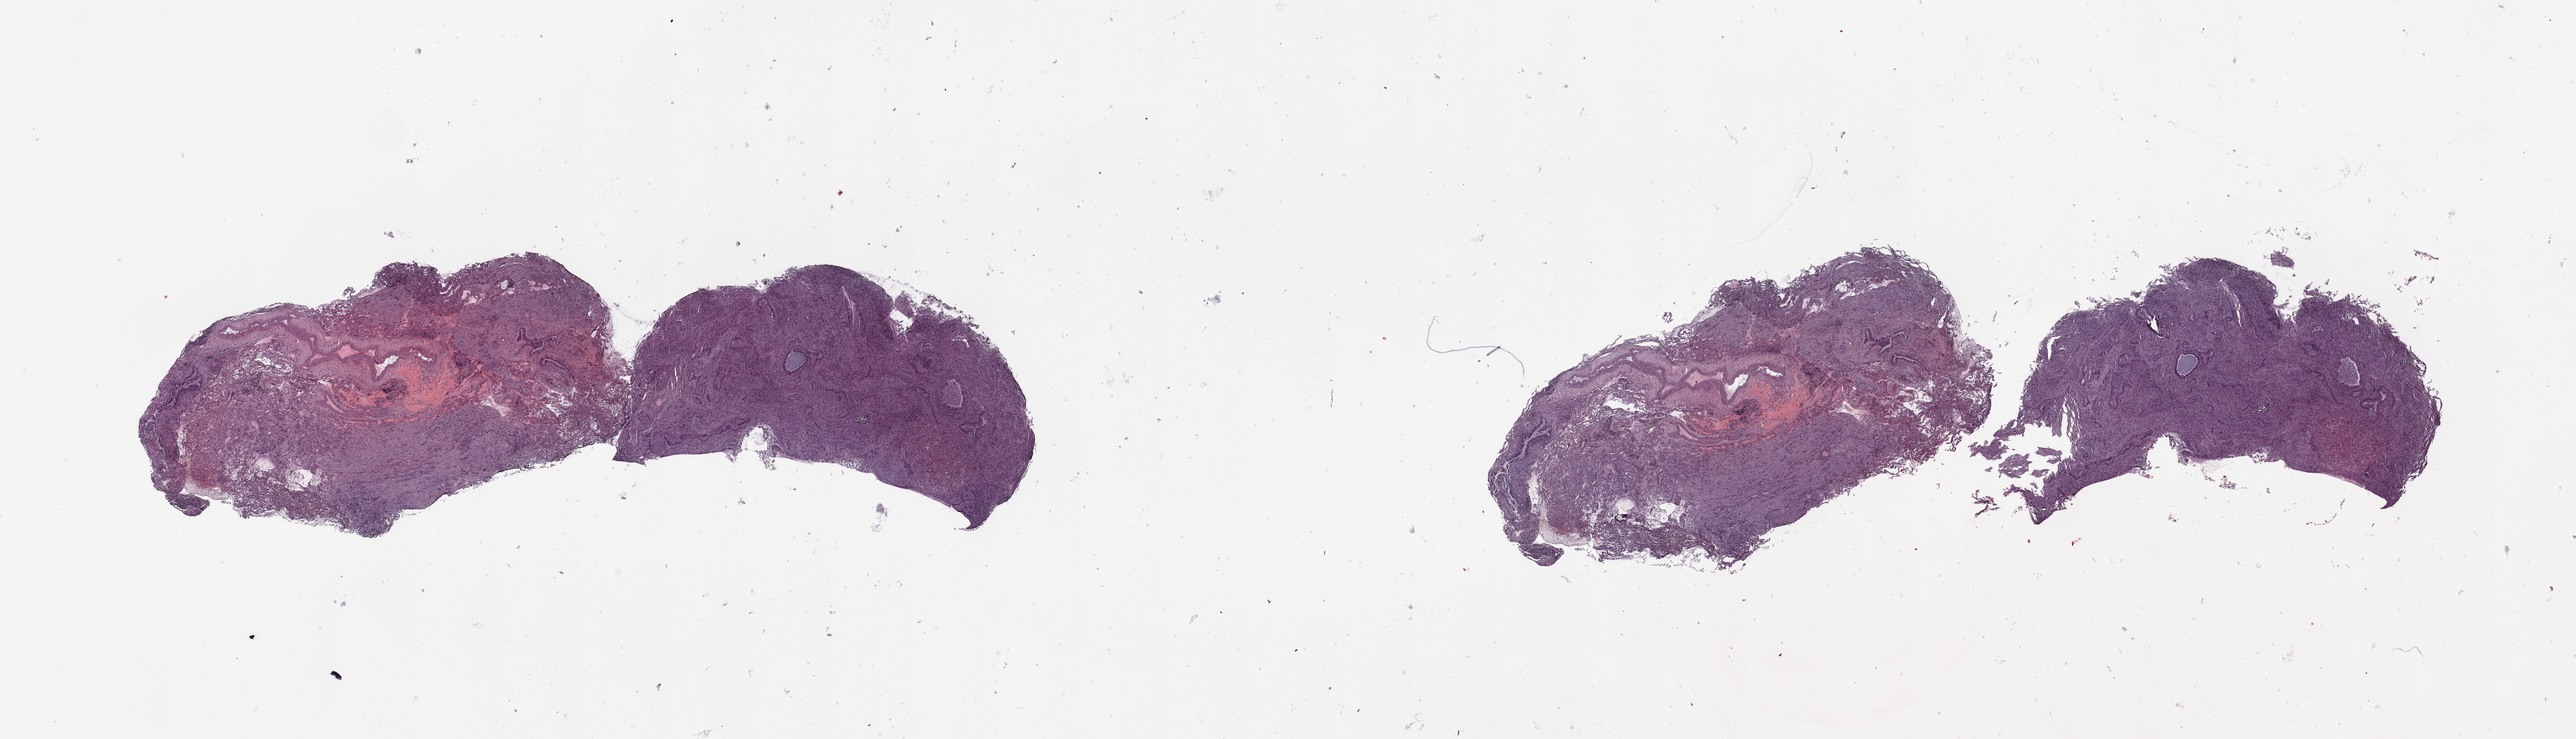
Digitized Hematoxylin and eosin (H&E) stained tissue section (whole slide) — shown as a low-resolution overview of the whole scanned area (about 30.5 x 8.8 mm, acquisition: 20x scan), tumour tissue sample, sampled site: lung. 55-year-old male patient. Histologic grade: G3 (poorly differentiated). Composition of this section per pathologist review: tumour nuclei 65%, necrosis 5%.
Diagnosis: Adenocarcinoma, NOS. Primary tumour site (as recorded): right upper lobe. AJCC pathologic stage: IV.